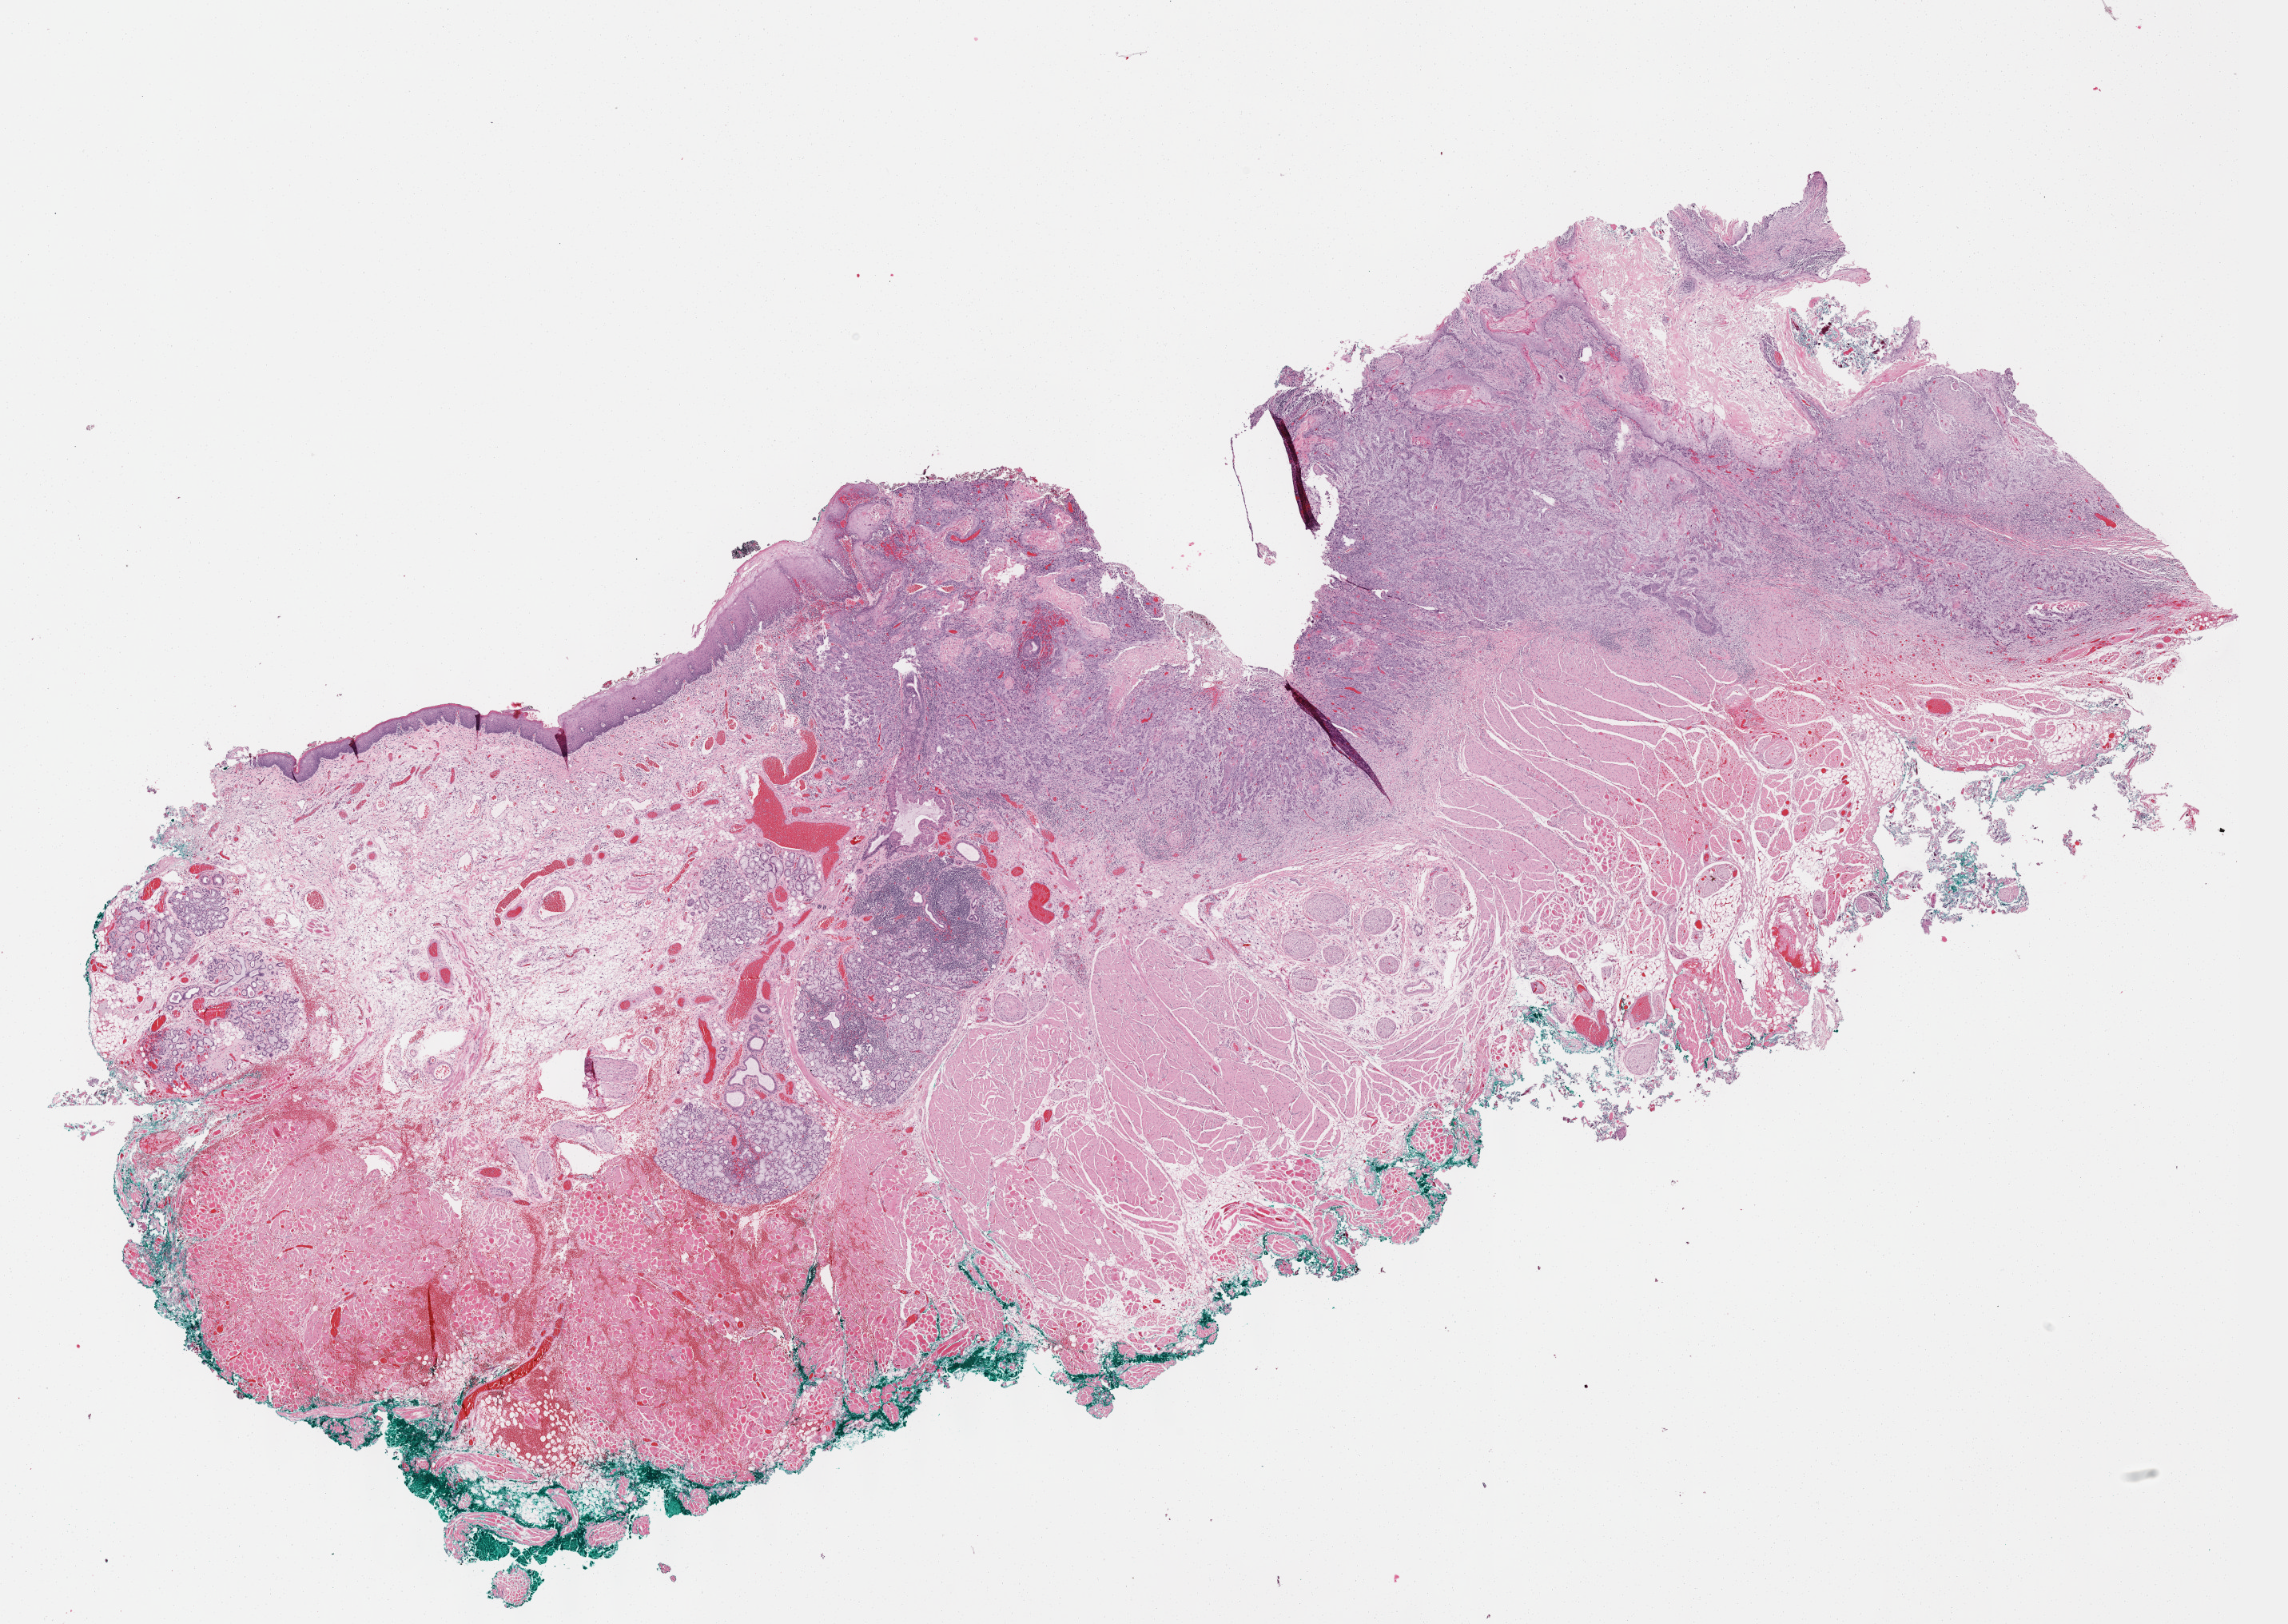
Digitized H&E-stained tissue section (whole slide), shown as a low-resolution overview of the whole scanned area (about 23.1 x 16.4 mm, slide scanned at 40x); formalin-fixed paraffin-embedded (FFPE) diagnostic section; sample: primary tumour, head and neck. Female, age 82 years at initial diagnosis. Histologic grade: G2 (moderately differentiated).
- lymph nodes positive (case pathology): 4 of 61 examined
- histologic diagnosis: Squamous cell carcinoma, keratinizing, NOS
- AJCC pathologic stage: IVA (7th edition)